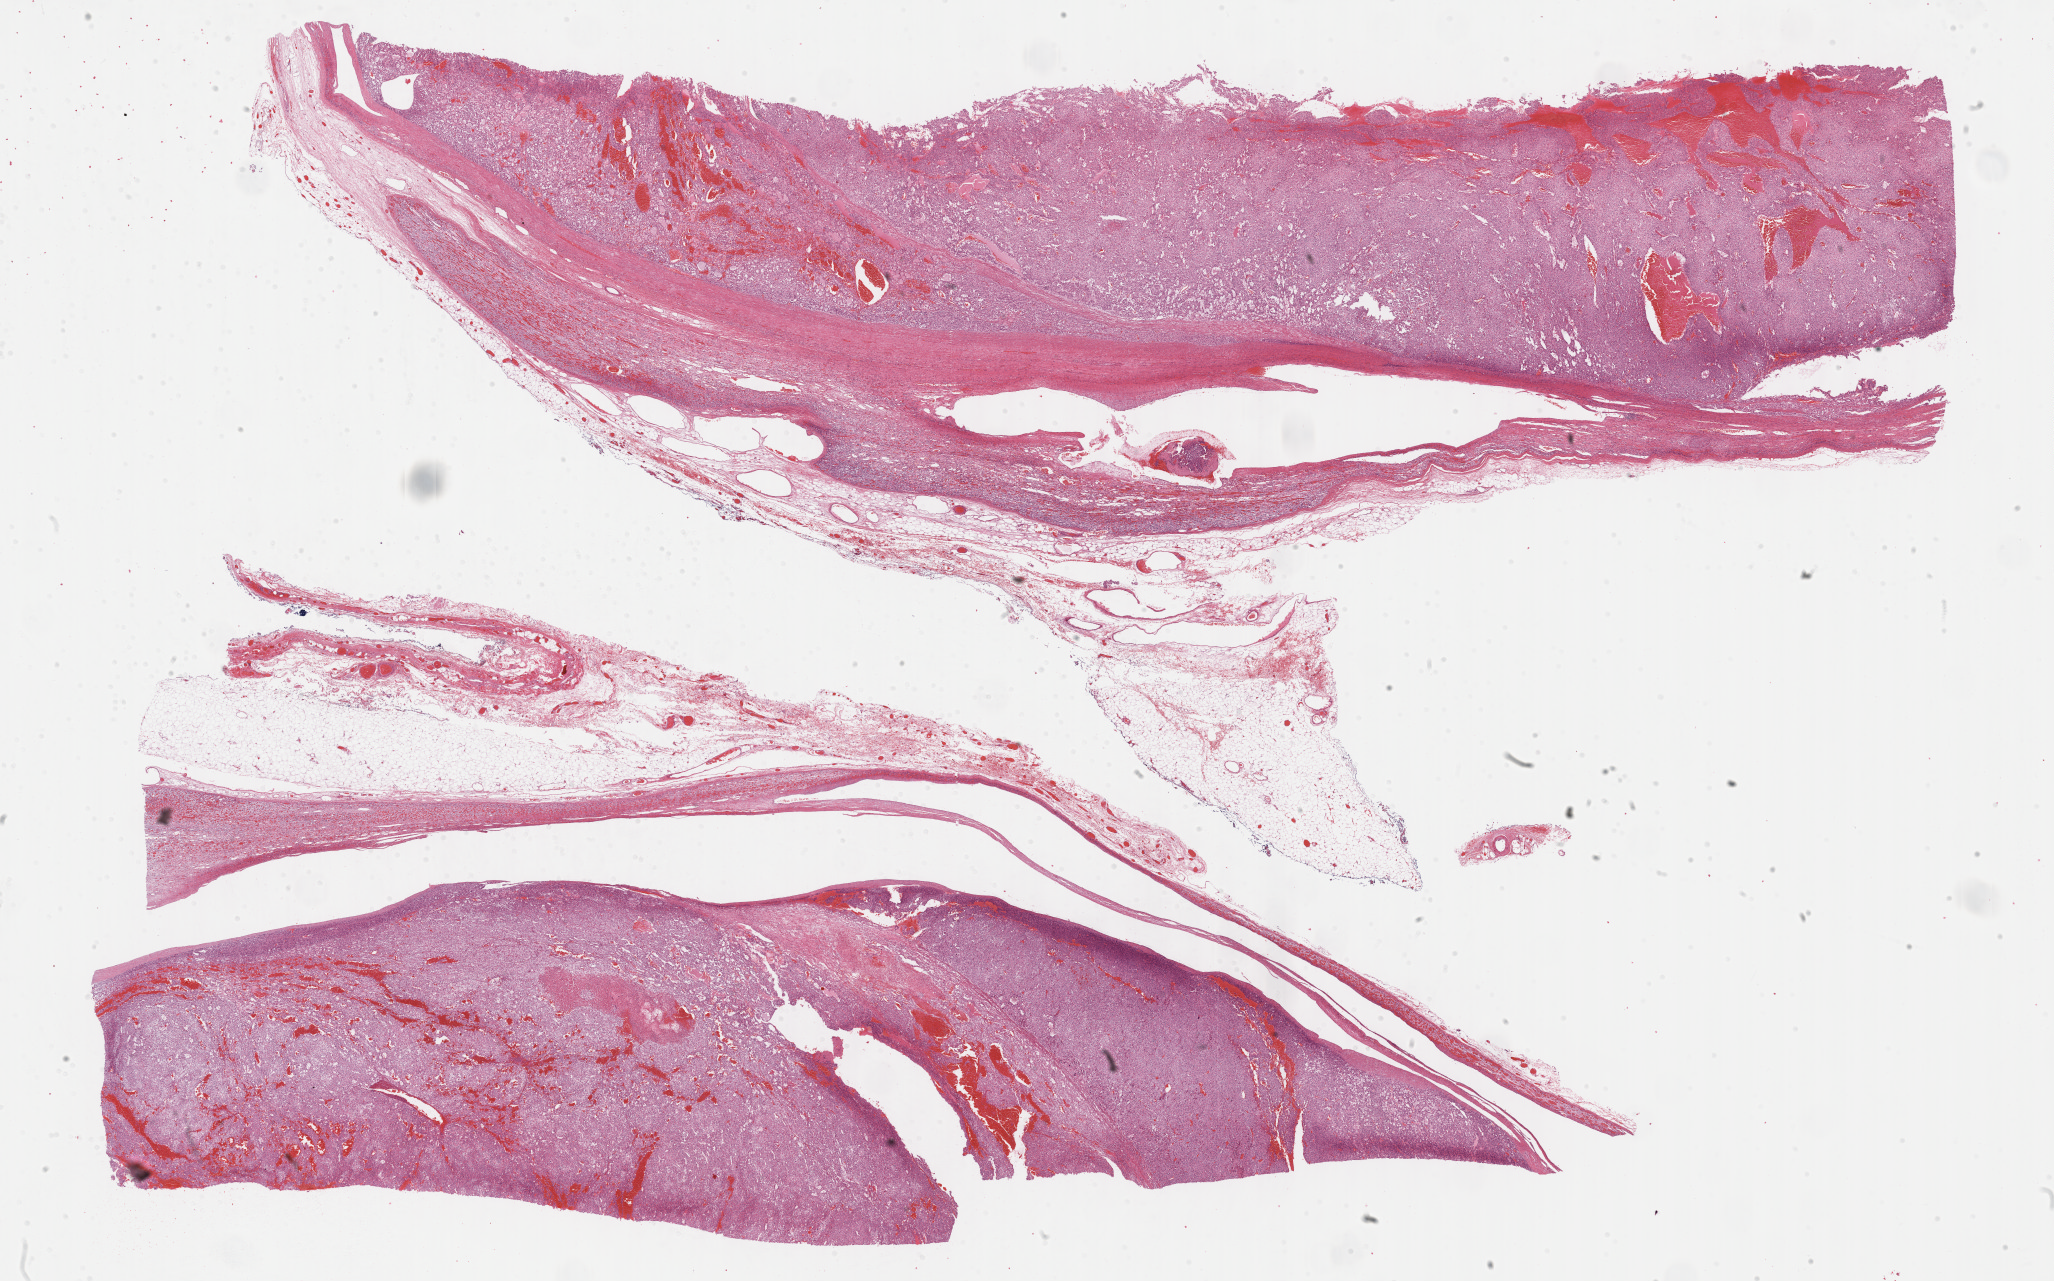
Whole-slide histology image, H&E-stained, whole scanned area (about 33.2 x 20.7 mm, acquisition: 40x scan) shown as a low-resolution overview; formalin-fixed paraffin-embedded (FFPE) diagnostic section; adrenal cortex, primary tumour sample. Male patient; age at initial diagnosis 37 years.
Pathologic diagnosis: Adrenal cortical carcinoma (cortex of adrenal gland). Laterality: left.